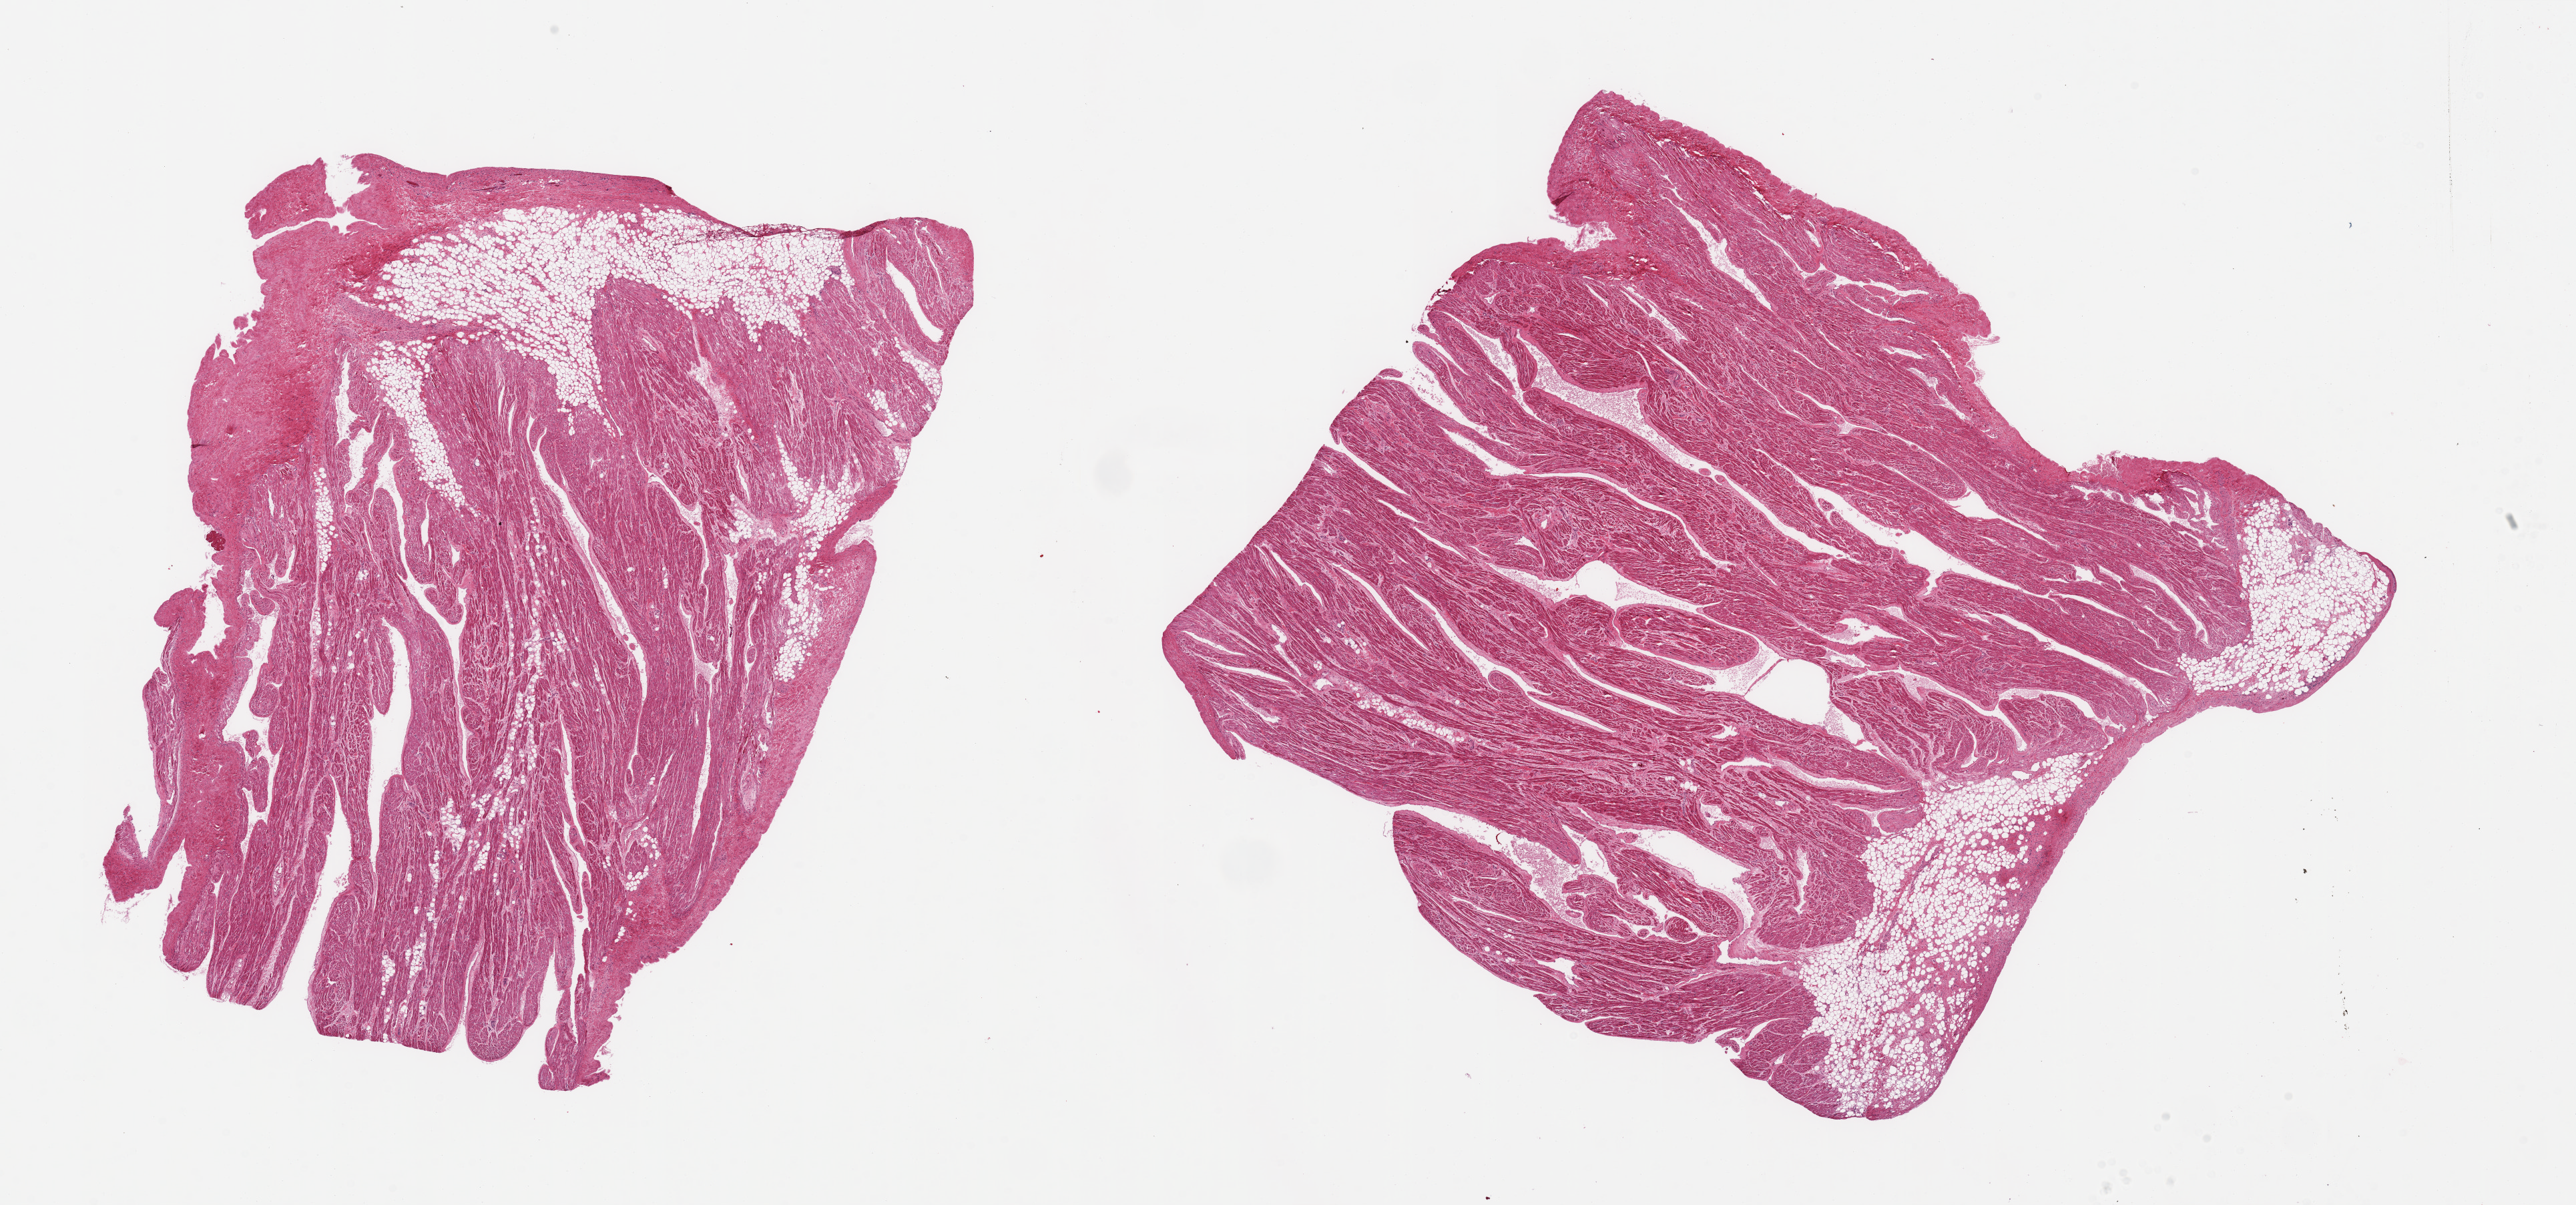
Haematoxylin and eosin whole-slide image, a low-resolution overview of the entire scanned area, about 30.5 x 14.3 mm (from a 20x scan), PAXgene-fixed paraffin-embedded (PFPE) section, target tissue: auricular appendage, tissue donor sample.
Pathologist's review note for this sample: 2 pieces; 10-20% fat/fibrous.